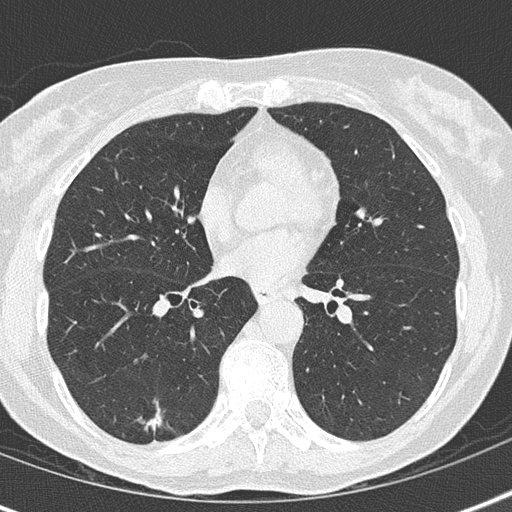
Low-dose screening chest CT, axial slice. Baseline screening round. Lung window (W 1500 / L -600 HU). 2 mm slice thickness. Lung (sharp) reconstruction kernel (B50f). Female, age 69 years at enrolment. Current smoker at enrolment.
Lesion marked by an expert reader, bounding box <118,394,181,452> (left, top, right, bottom; pixels). The screening reader recorded 2 non-calcified nodules or masses ≥4 mm on this exam (right lower lobe, left lower lobe); which of them this box marks is not recorded. Official screen result: positive, change unspecified: nodule(s) >= 4 mm or enlarging nodule(s), mass(es), or other non-specific abnormalities suspicious for lung cancer. Lung cancer was diagnosed 476 days after this screen (after the second annual screen): adenocarcinoma, NOS, right lower lobe, moderately differentiated (G2), stage IA (AJCC 6th edition), 16 mm at pathology.